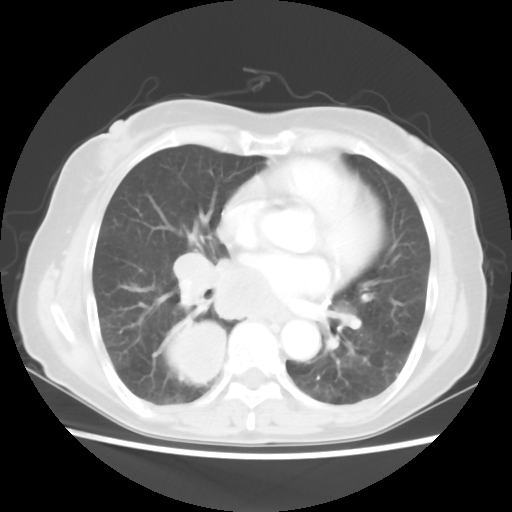
Chest CT, one axial slice. Slice 28 of 56 in the series (ordered by position). Reconstruction kernel STANDARD. 120 kVp. Lung window (W 1500 / L -600 HU). 512 × 512 image matrix, field of view 332 × 332 mm. Patient: female, 66 years. From the clinical record (not read from this slice): clinical TNM (as recorded): T2 N3 M0; histopathological grade: G3.
Outlined on this slice (rectangle marked by the reading radiologist):
- lung tumour (recorded histology: small cell carcinoma): box from (x=163, y=317) to (x=237, y=392) px